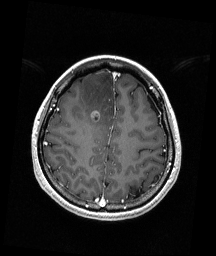
Brain MRI from a brain-tumour surgery series, one axial slice; slice 55 of 192 in the series (ordered by position); T1-weighted post-contrast; 216 × 256 image matrix, field of view 211 × 250 mm. Case-level facts recorded for this patient, not image findings: histopathology: Astrocytoma; WHO grade: 4; IDH mutation: yes; tumour location: Right Frontal.
Annotated regions visible in this slice (manually delineated by an expert):
- tumour: bounding box [x1, y1, x2, y2] px = [91, 109, 100, 122]